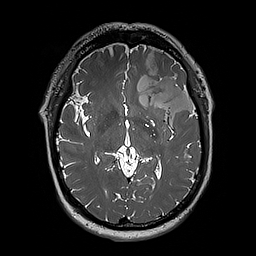
Brain MRI from a brain-tumour surgery series, one axial slice. 256 × 256 image matrix, field of view 250 × 250 mm. Case-level facts recorded for this patient, not image findings: histopathology: Oligodendroglioma; WHO grade: 3; IDH mutation: yes.
Outlined on this slice (manually delineated by an expert):
- tumour: bounding box <124,49,197,125> (left, top, right, bottom; pixels)